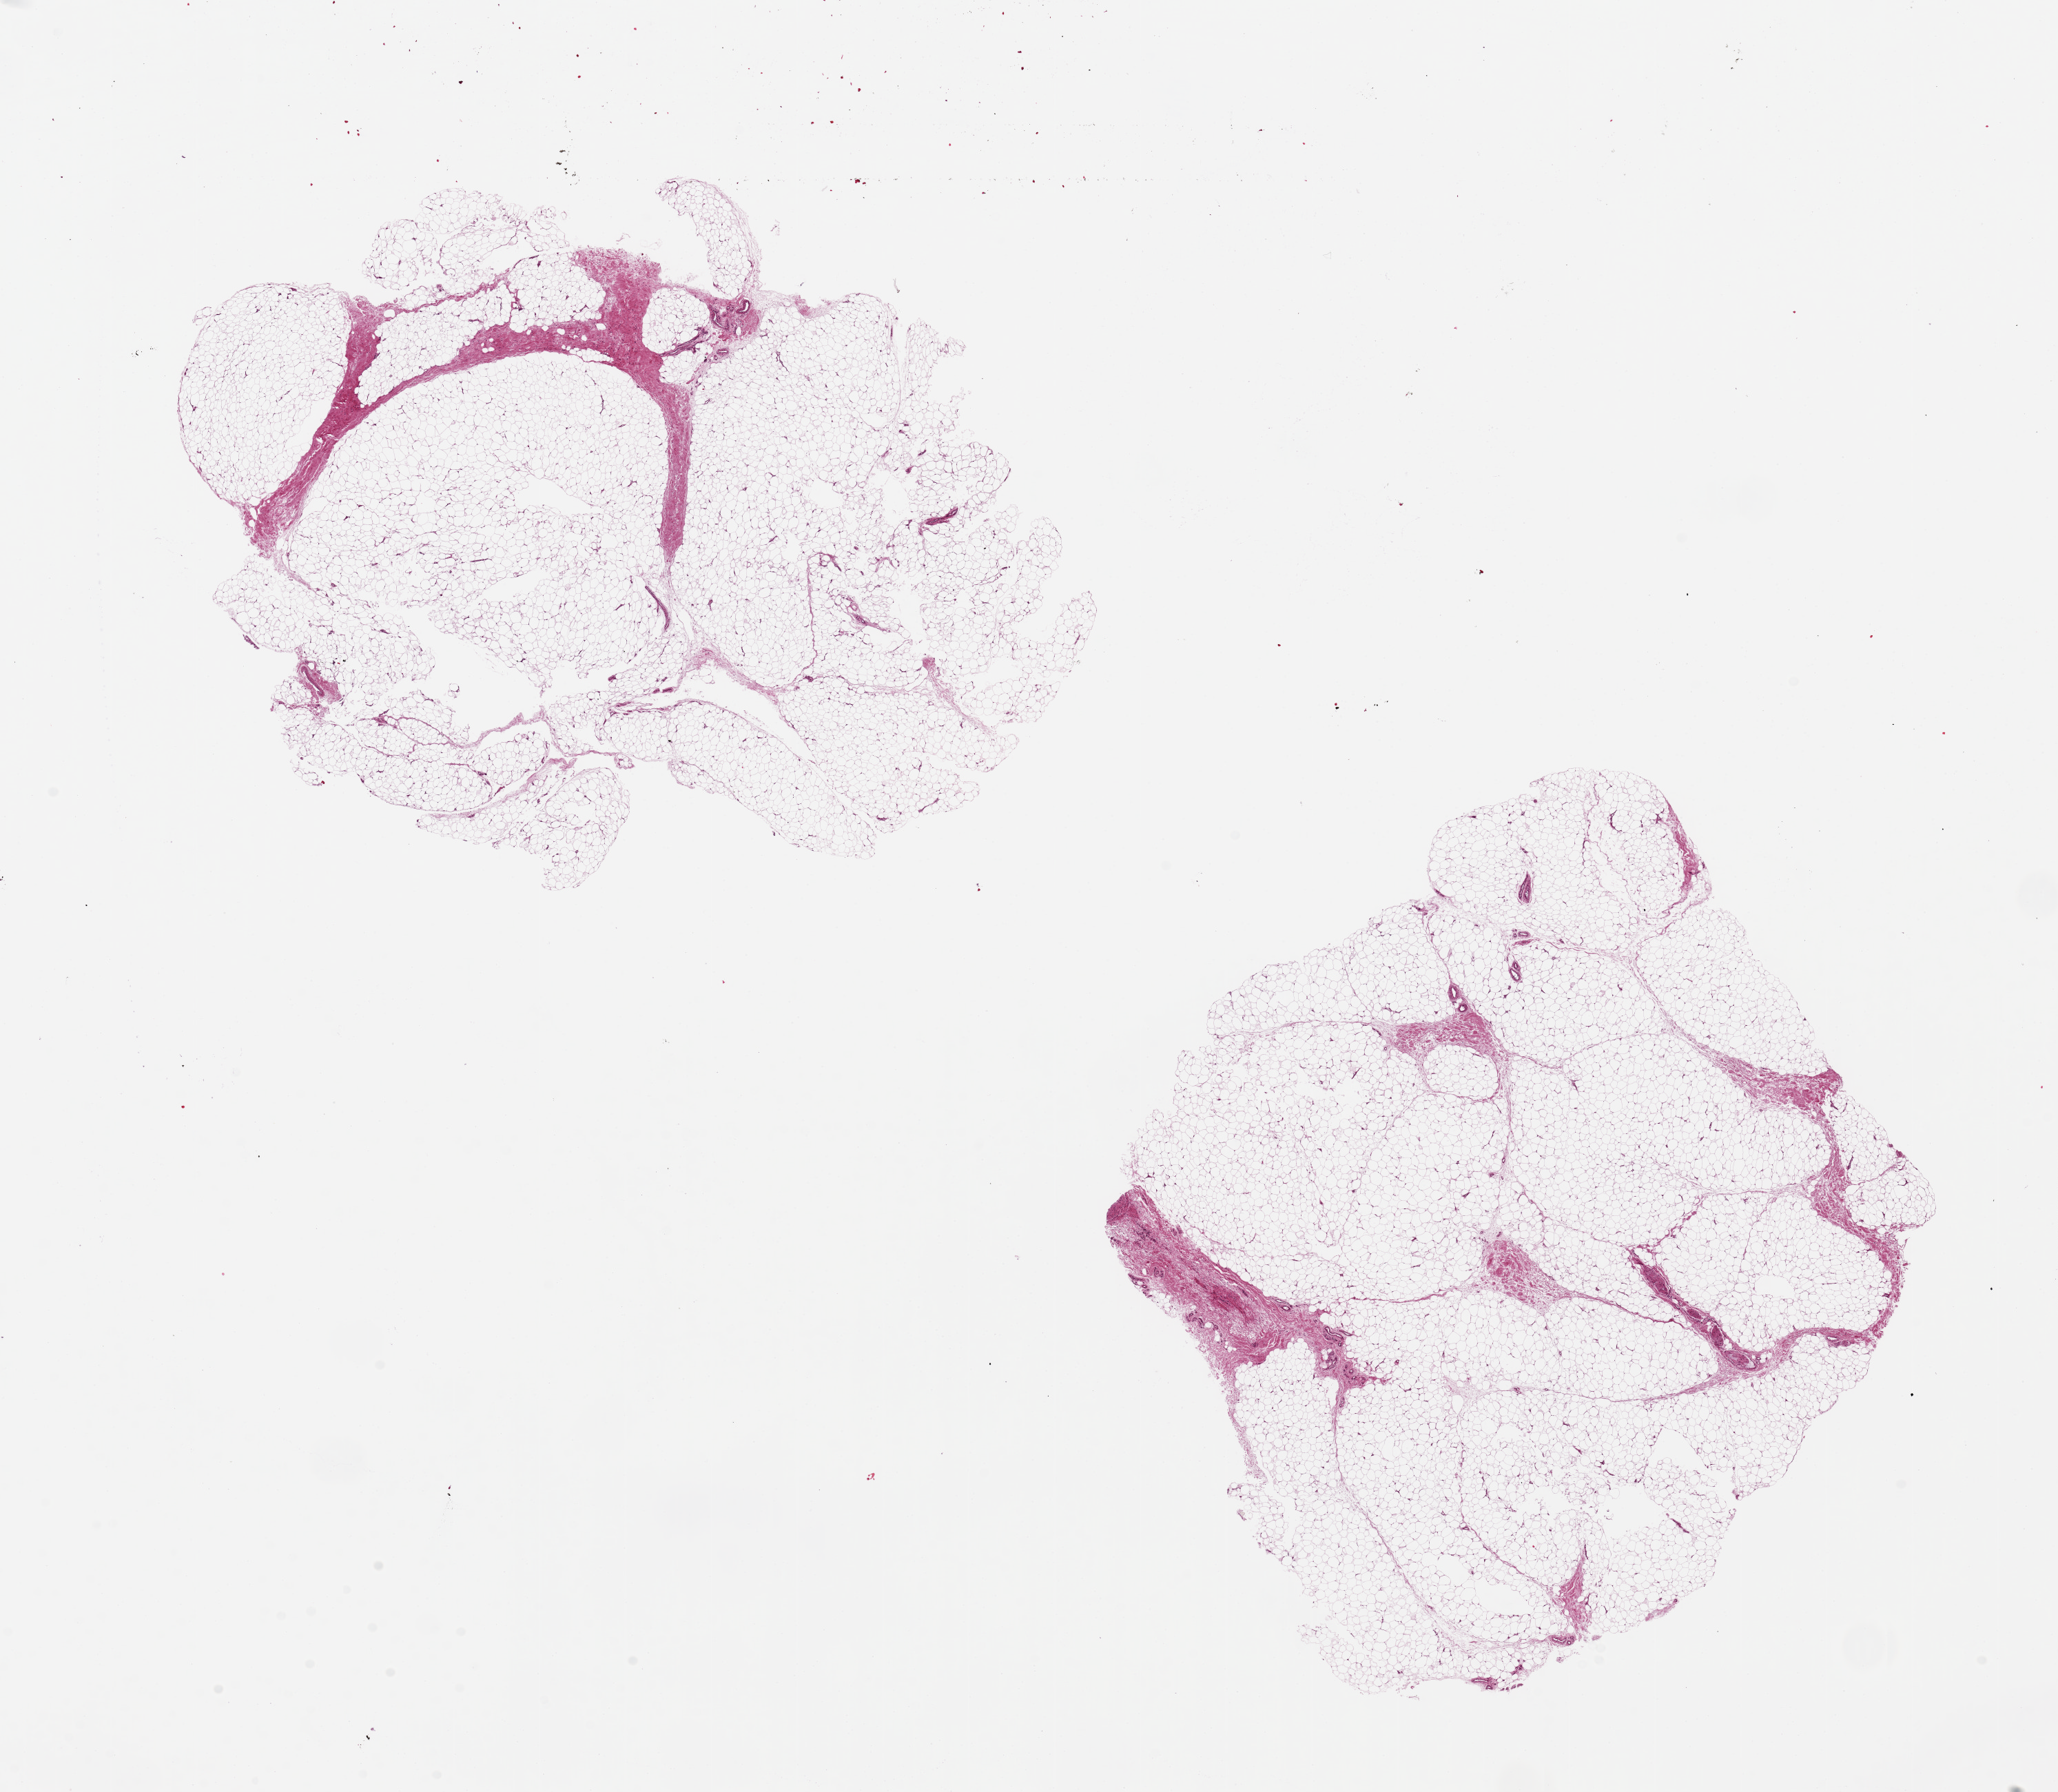
Hematoxylin and eosin (H&E) whole-slide image, a low-resolution overview of the entire scanned area, about 23.6 x 20.6 mm (acquisition: 20x scan); PAXgene-fixed paraffin-embedded (PFPE) section; section of adipose tissue (target tissue); tissue donor sample. Donor: male.
Pathologist's review note for this sample: 2 pieces, 11x8 & 9x9mm; well fixed.